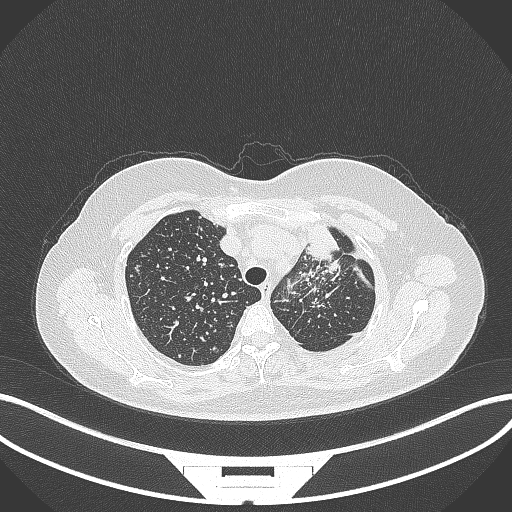
Chest CT, one axial slice. Position 267 of 348 along the scan axis. Lung window (W 1500 / L -600 HU). 1 mm slice thickness. 512 × 512 image matrix, field of view 400 × 400 mm. Patient: female, 49 years. Case-level facts recorded for this patient, not image findings: clinical TNM (as recorded): T1c N0 M1.
Outlined on this slice (bounding box drawn by a radiologist):
- lung tumour (recorded histology: adenocarcinoma): bounding box <299,216,344,262> (left, top, right, bottom; pixels)